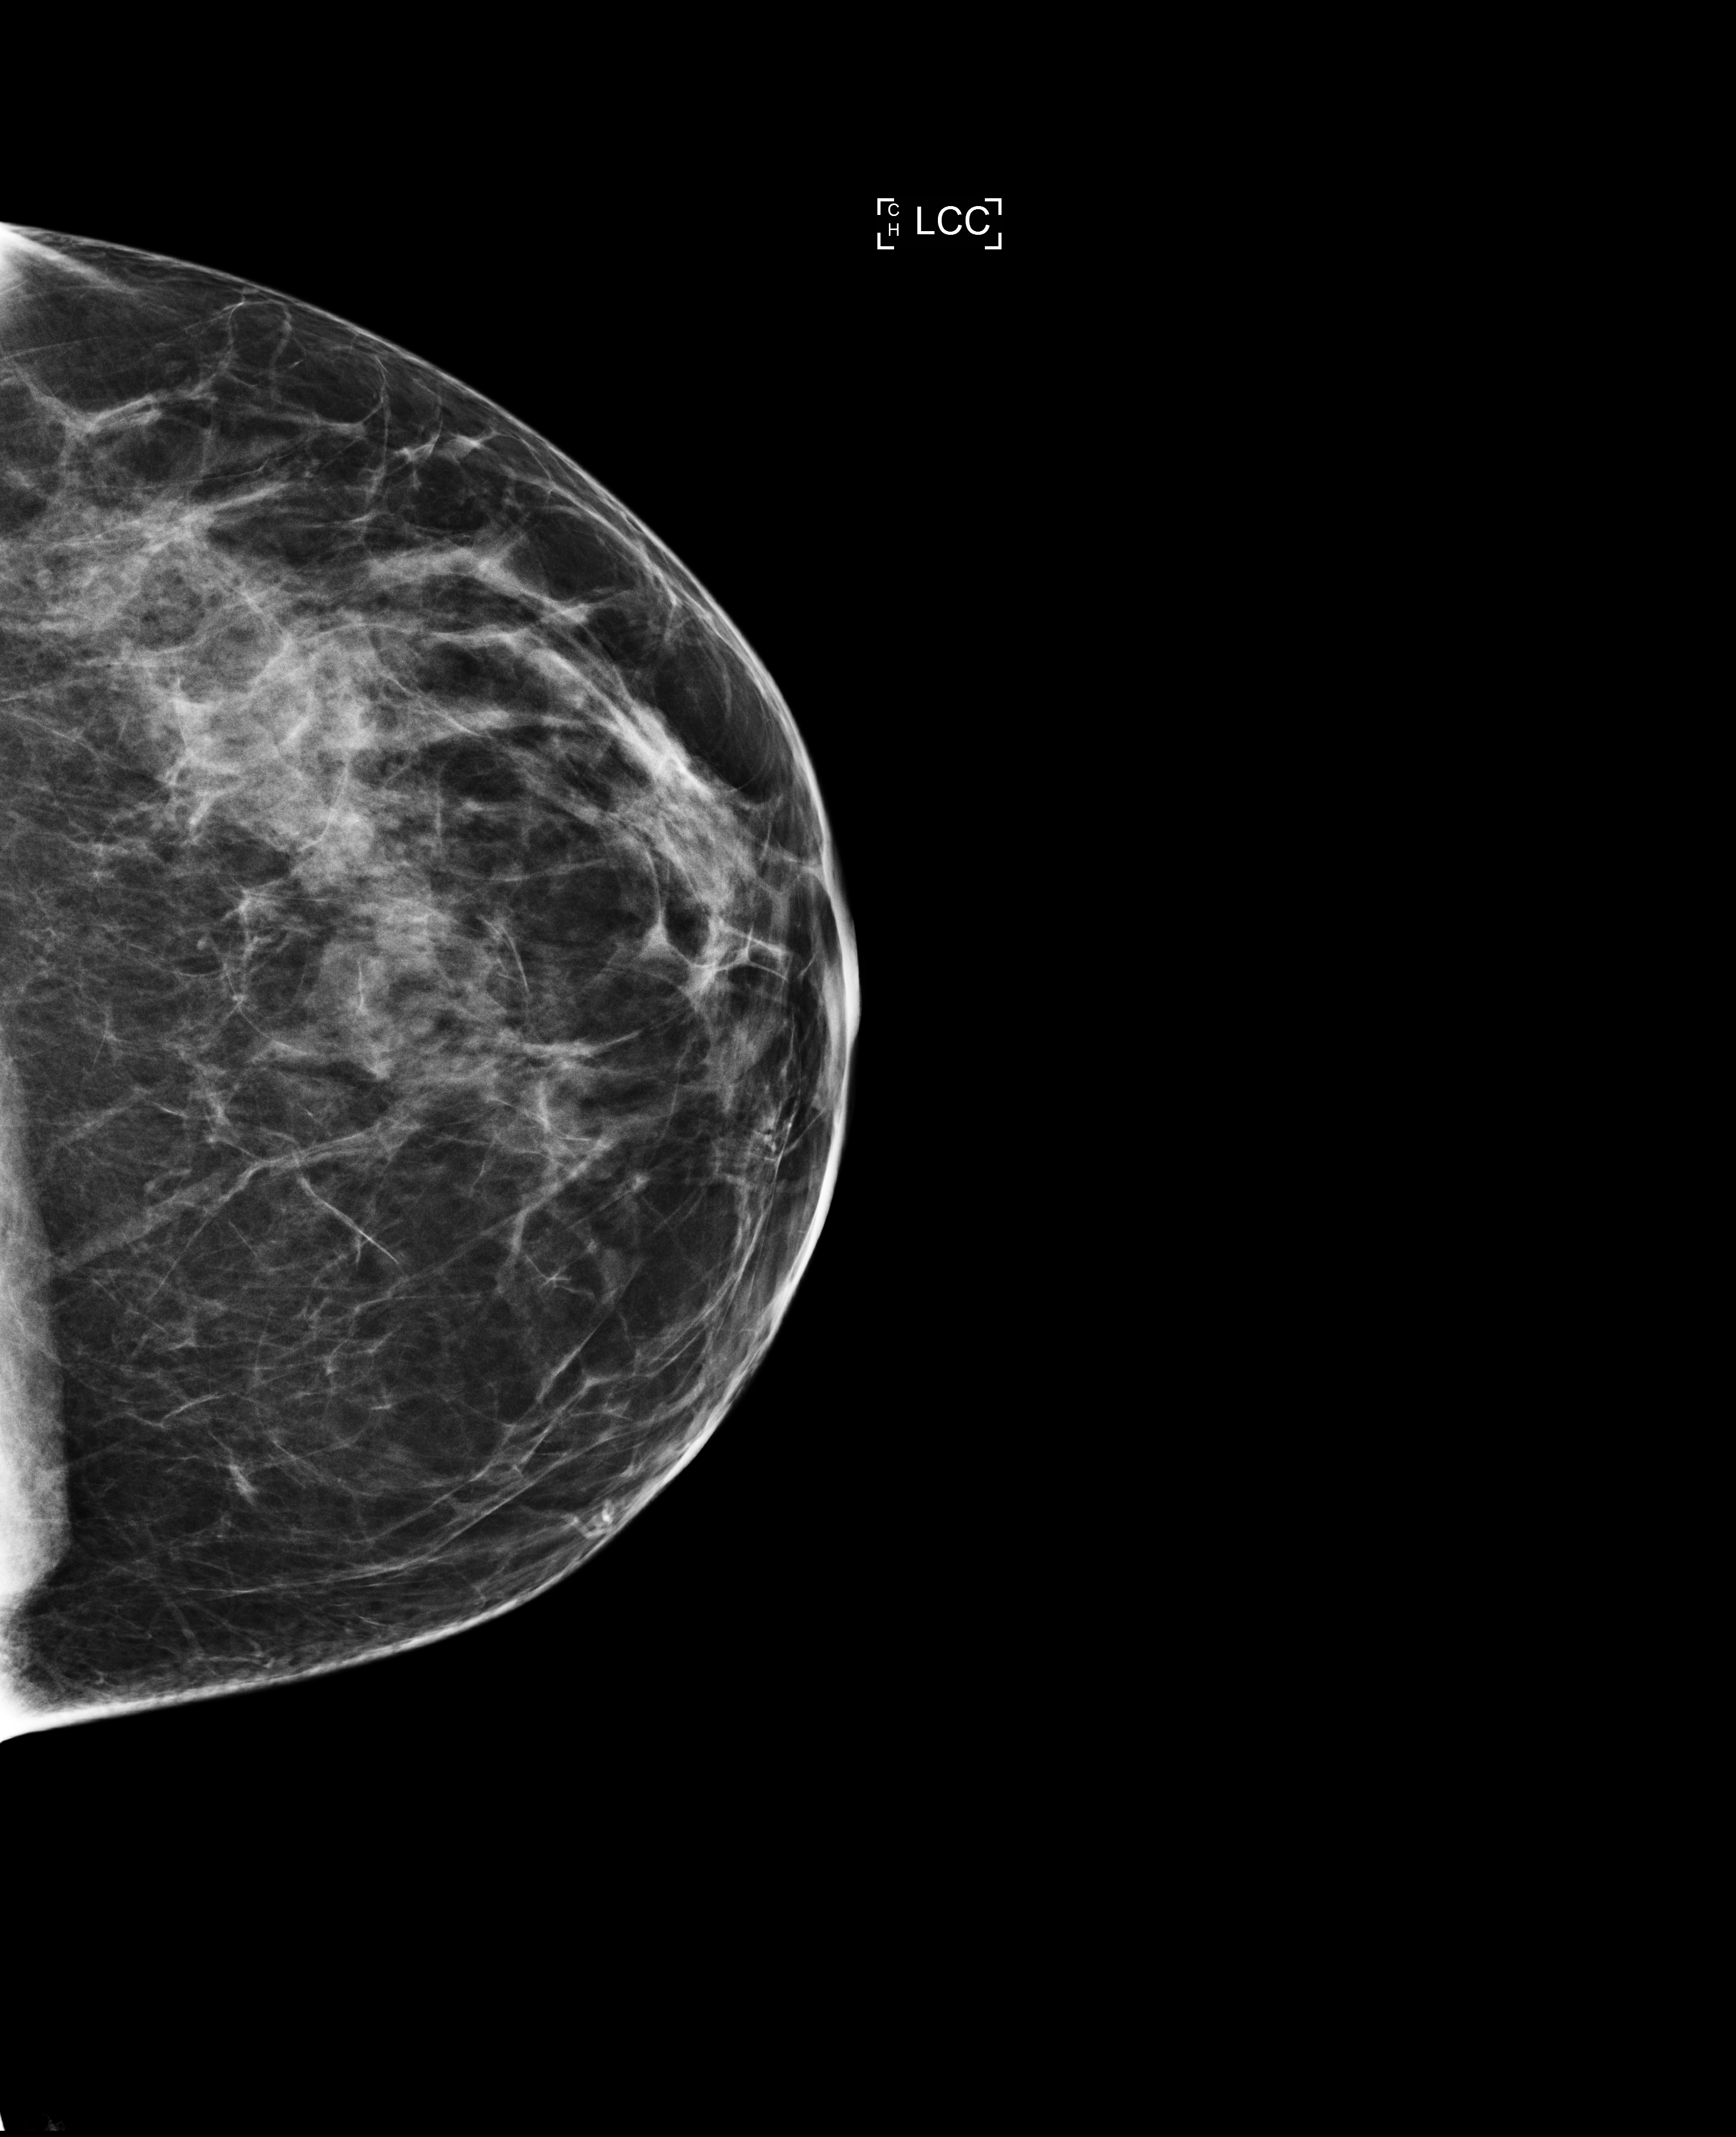
Digital mammogram (FFDM); left breast; cranio-caudal projection; annual screening mammography examination; compressed breast thickness 65 mm; system: Selenia Dimensions. Patient: female, 40 years.
- BI-RADS breast density category at the screening exam (both breasts, scale 1–4): 2
- final BI-RADS category for the screening round (tomosynthesis exam, both breasts): category 1
- recall: no recall after this screen